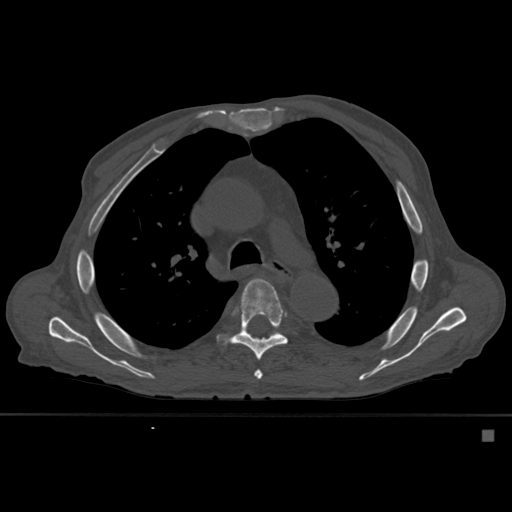
CT including the spine, one axial slice; slice 386 of 527 in the series (ordered by position); bone window (W 1800 / L 400 HU); 1.5 mm slice thickness; 512 × 512 image matrix, field of view 373 × 373 mm. Patient: male, 78 years. Case-level facts recorded for this patient, not image findings: primary cancer: prostate.
Annotated regions visible in this slice (semi-automatically segmented with operator editing):
- T5 vertebra: bounding box <243,344,262,380> (left, top, right, bottom; pixels)
- T6 vertebra: <230,278,288,361>